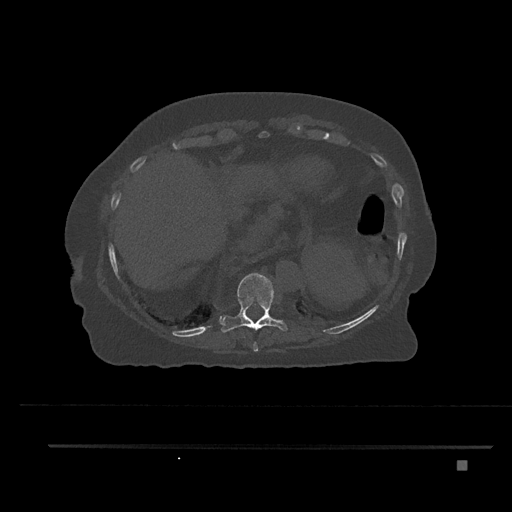
CT including the spine, one axial slice; slice 357 of 797 in the series (ordered by position); reconstruction kernel Br40s/3; 120 kVp; bone window (W 1800 / L 400 HU); 0.5 mm slice thickness; 512 × 512 image matrix. Female patient, age 76 years. From the clinical record (not read from this slice): primary cancer: lung; vertebrae with lytic lesions (as recorded): T11, L3.
Outlined on this slice (semi-automatic segmentation, software-assisted and operator-edited):
- T10 vertebra: bounding box [x1, y1, x2, y2] px = [220, 273, 288, 333]
- T9 vertebra: [253, 341, 259, 352]